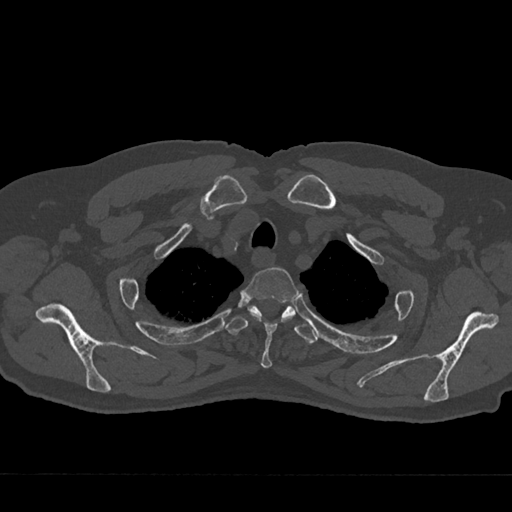
CT including the spine, one axial slice; slice 592 of 797 in the series (ordered by position); reconstruction kernel Br40s/3; 120 kVp; bone window (W 1800 / L 400 HU); 512 × 512 image matrix, field of view 377 × 377 mm. Male patient, age 75 years. From the clinical record (not read from this slice): primary cancer: renal.
Outlined on this slice (semi-automatic segmentation, software-assisted and operator-edited):
- T2 vertebra: bounding box [x1, y1, x2, y2] px = [242, 267, 298, 368]
- T3 vertebra: [226, 306, 318, 344]